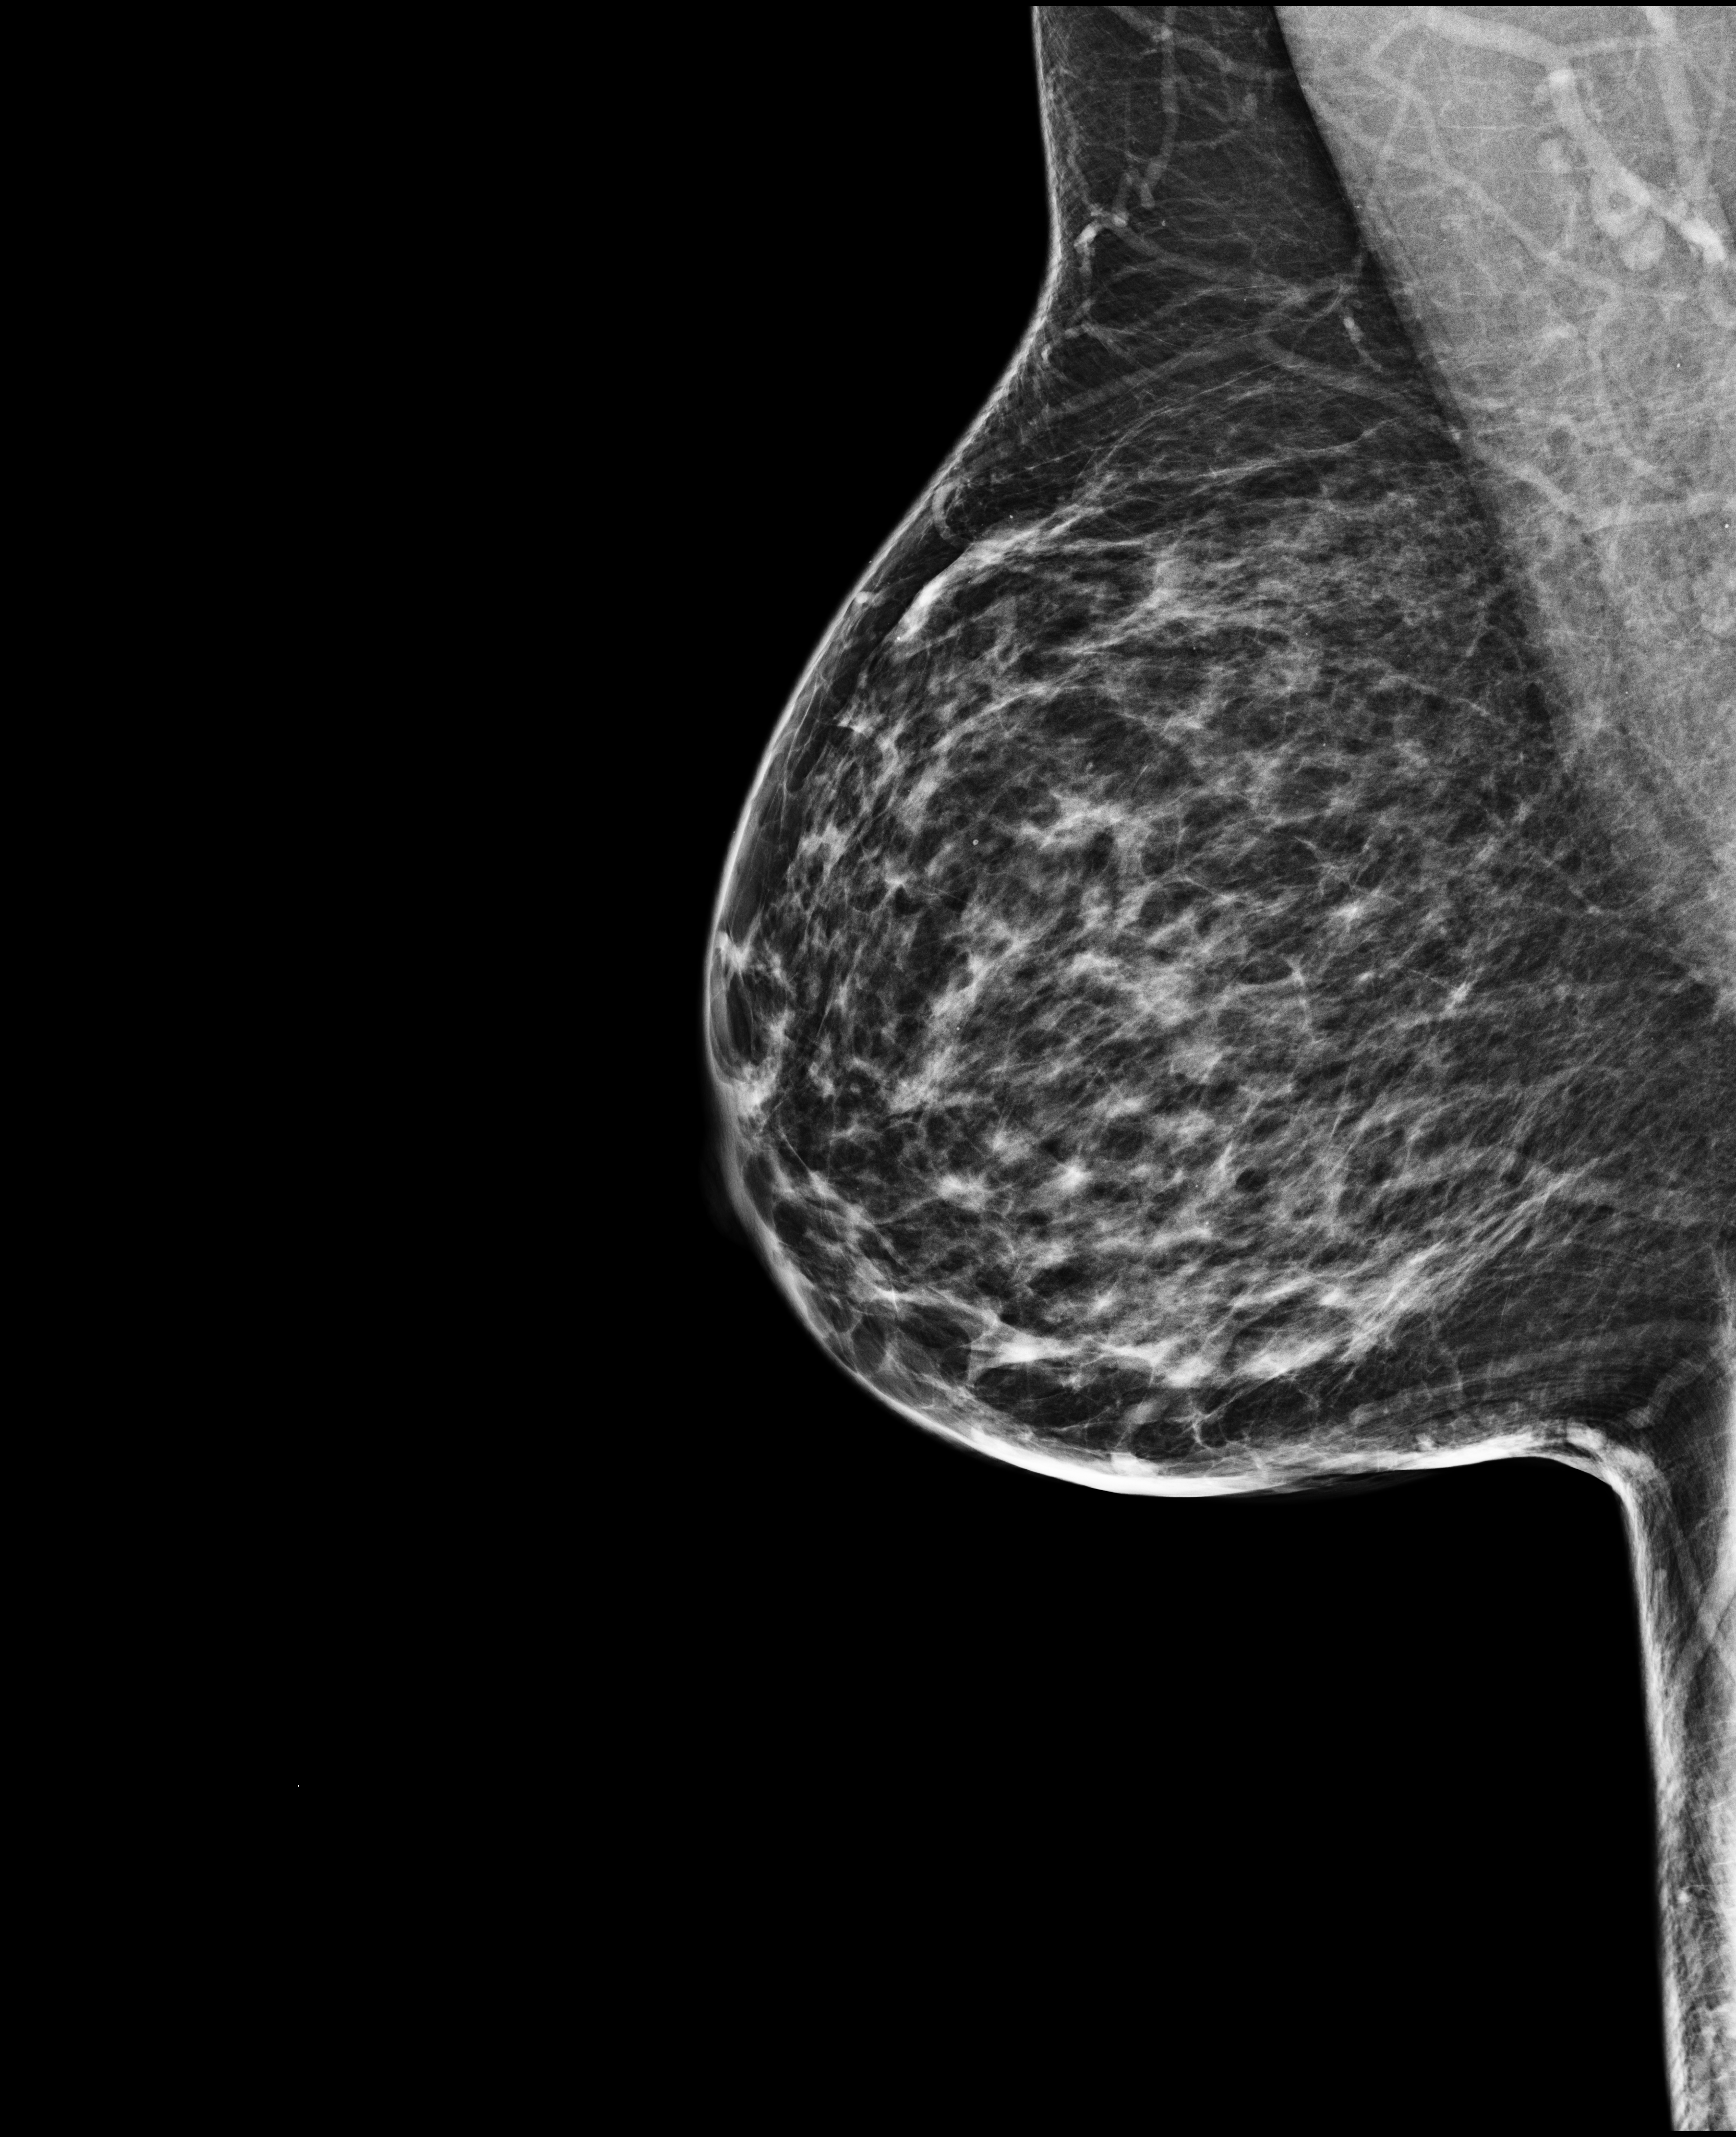
Digital mammogram (FFDM); right breast; mediolateral oblique (MLO) view; annual screening mammography examination. Patient aged 47 years (female).
- BI-RADS breast density category at the screening exam (both breasts, scale 1–4): 3
- final BI-RADS assessment for this screening round (tomosynthesis exam, both breasts): category 1
- recall: no recall after this screen